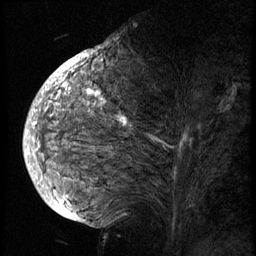
Breast MRI (dynamic contrast-enhanced), one sagittal slice. Position 35 of 74 along the scan axis. 3 images stored at this slice position (order not interpretable as contrast timing). 1.5 T. TE 4.2 ms, TR 8.9 ms. 256 × 256 image matrix, field of view 200 × 200 mm. Female patient, age 57 years. Case-level facts recorded for this patient, not image findings: setting: breast cancer imaged before/during neoadjuvant chemotherapy; receptor status: HER2-positive.
Annotated regions visible in this slice (semi-automatic segmentation, software-assisted and operator-edited):
- analysis volume of interest (the breast-tissue region the enhancement analysis was run in; not a lesion): box from (x=40, y=62) to (x=237, y=175) px
- tumour enhancement mask (voxels above the 140 % enhancement threshold inside the analysis volume of interest): (x=40, y=66)–(x=186, y=173)